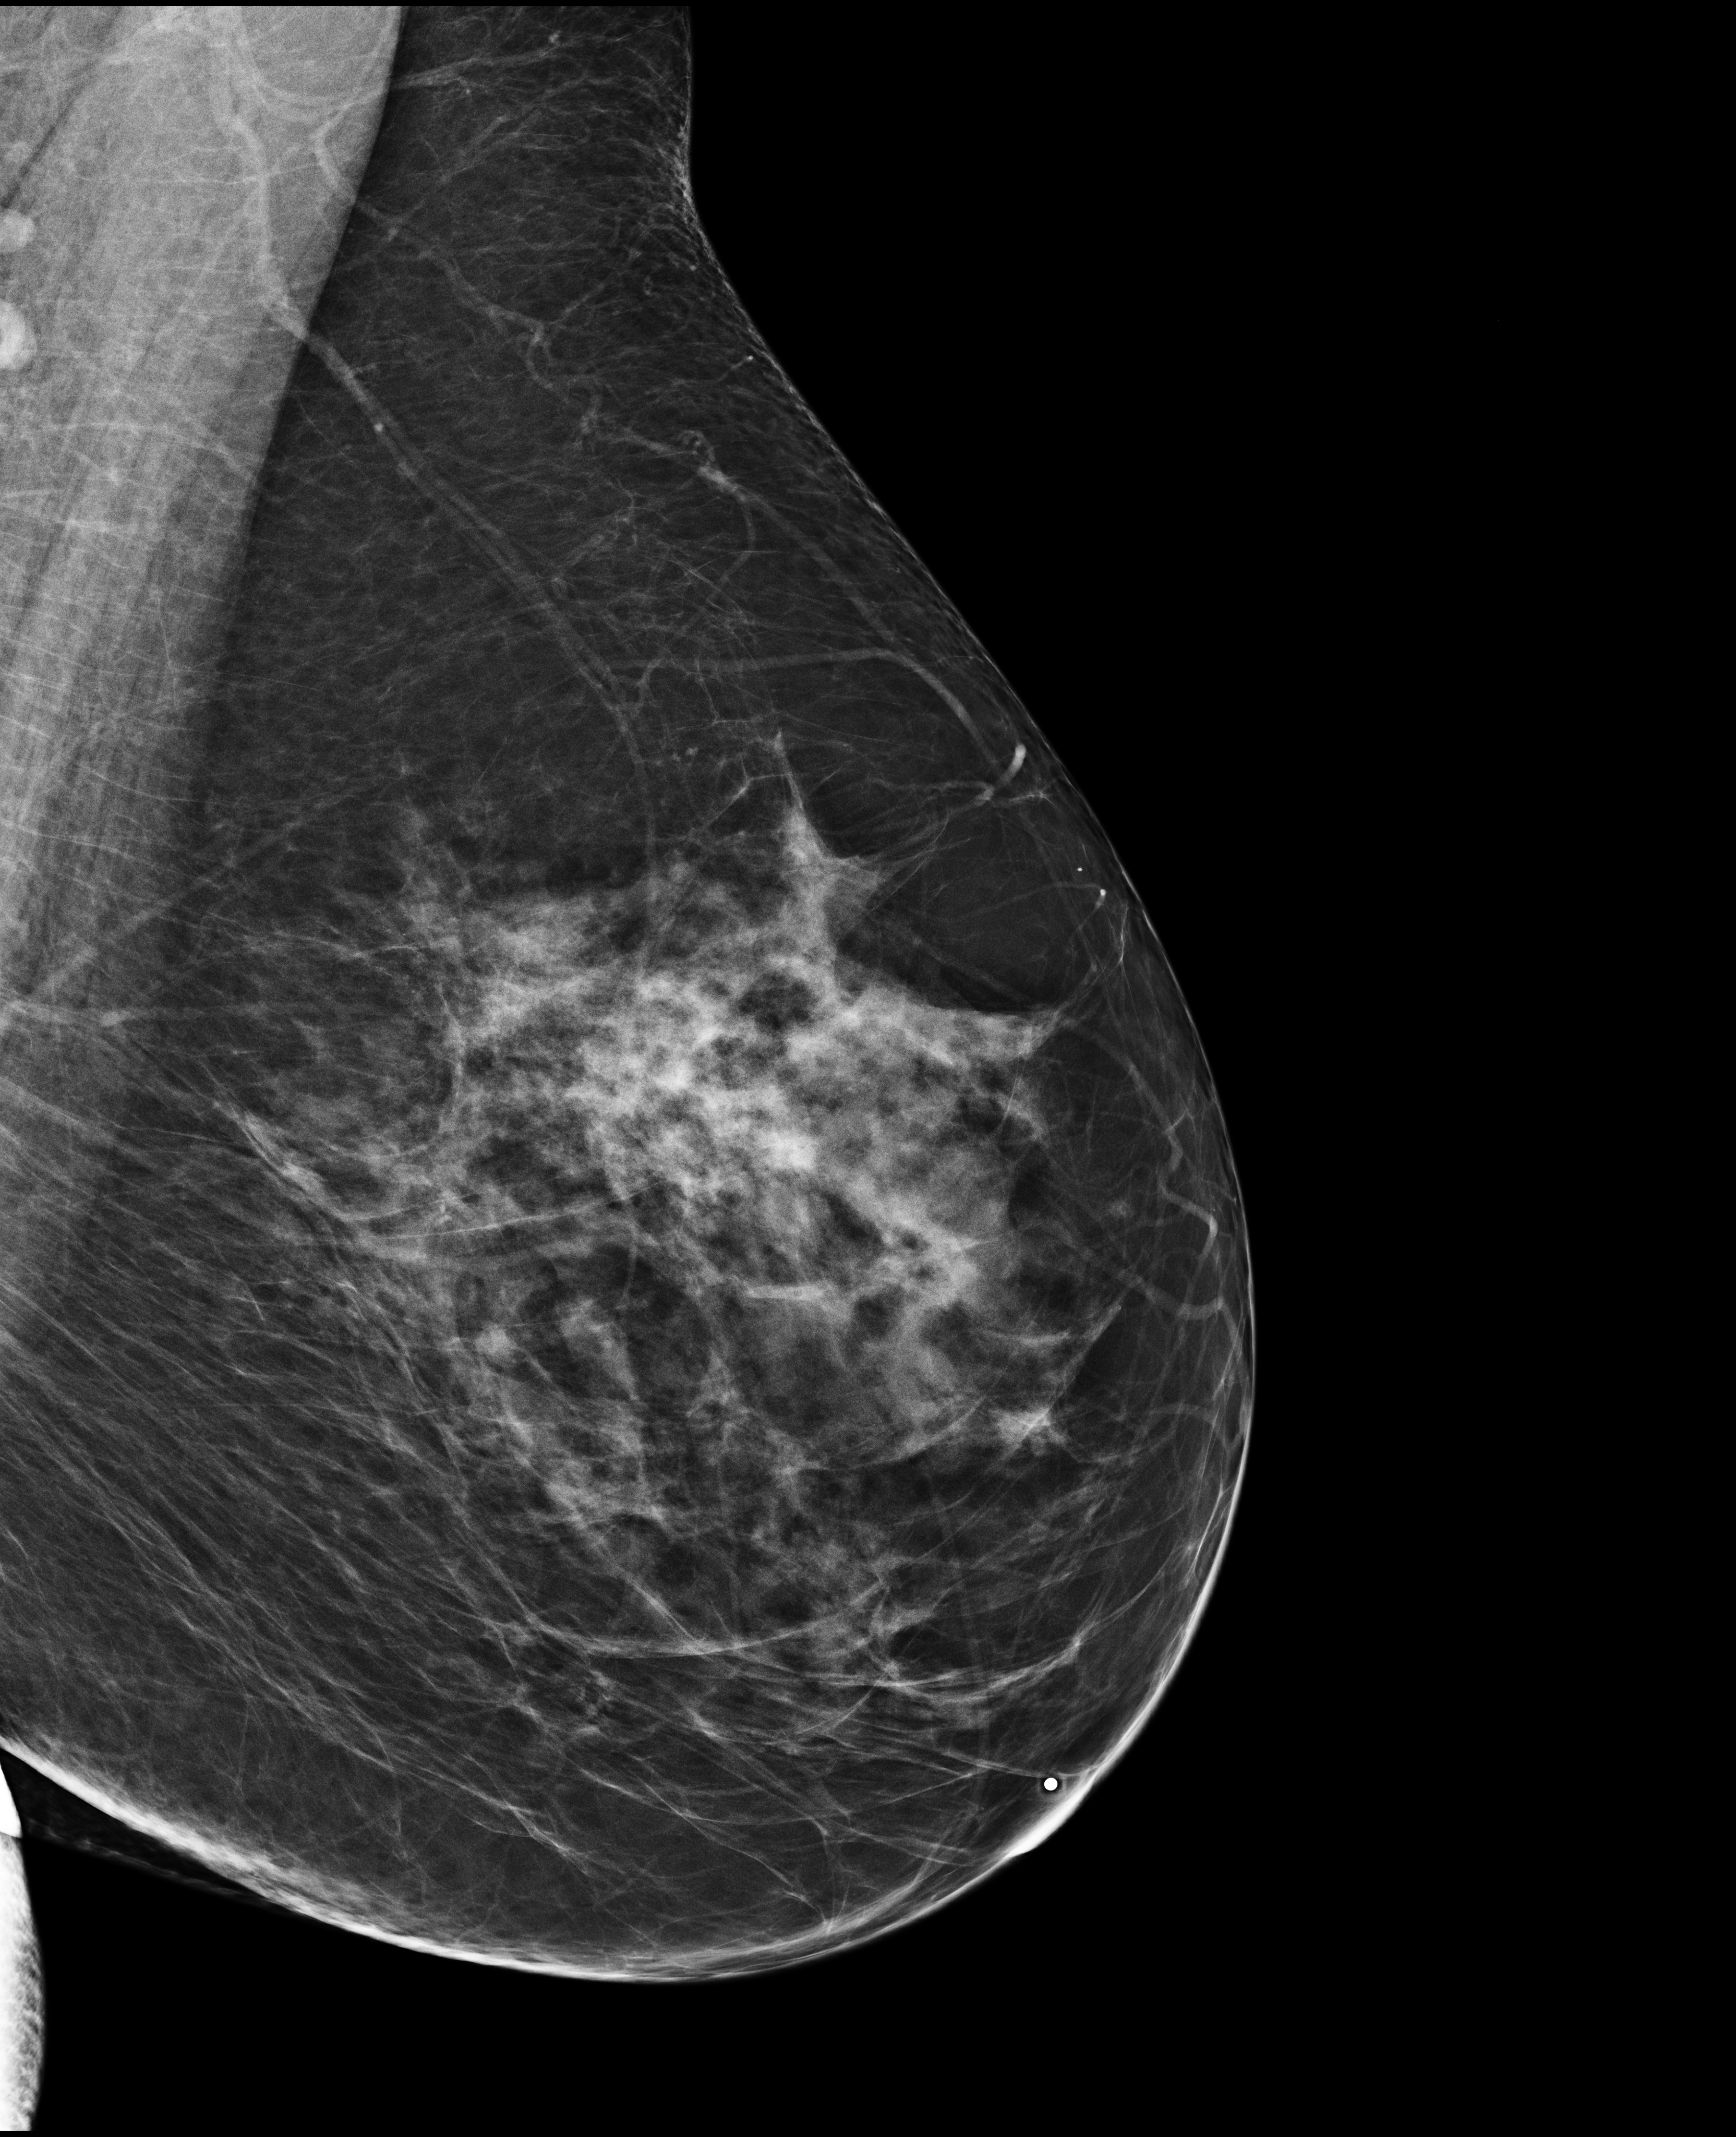
Annual screening mammography examination, system: Selenia Dimensions. Female patient, age 60 years.
Image type: full-field digital mammogram. Breast: left. Projection: medio-lateral oblique projection. BI-RADS breast density category at the screening exam (both breasts, scale 1–4): 3. Final BI-RADS category for the screening round (tomosynthesis exam, both breasts): category 1. Recall: no recall after this screen.